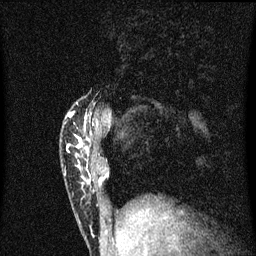
Breast MRI (dynamic contrast-enhanced), one sagittal slice. Position 14 of 60 along the scan axis. Dynamic contrast-enhanced series, image 2 of 3 at this slice position (ordered by acquisition). 1.5 T. TE 4.2 ms, TR 8.4 ms. 2 mm slice thickness. 256 × 256 image matrix, field of view 200 × 200 mm. Patient: female, 40 years.
Outlined on this slice (semi-automatically segmented with operator editing):
- analysis volume of interest (the breast-tissue region the enhancement analysis was run in; not a lesion): bounding box <62,102,102,195> (left, top, right, bottom; pixels)
- tumour enhancement mask (voxels above the 70 % enhancement threshold inside the analysis volume of interest): <69,112,92,177>